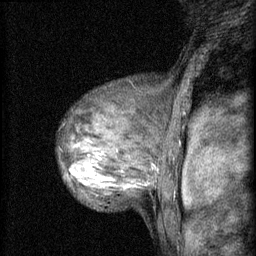
Breast MRI (dynamic contrast-enhanced), one sagittal slice. Position 46 of 60 along the scan axis. 3 images stored at this slice position (order not interpretable as contrast timing). 1.5 T. TE 4.2 ms, TR 8.2 ms. 256 × 256 image matrix, field of view 180 × 180 mm. Patient: female, 48 years.
Annotated regions visible in this slice (semi-automatic segmentation, software-assisted and operator-edited):
- analysis volume of interest (the breast-tissue region the enhancement analysis was run in; not a lesion): bounding box (x1, y1, x2, y2) in pixels: (60, 138, 133, 191)
- tumour enhancement mask (voxels above the 70 % enhancement threshold inside the analysis volume of interest): (70, 156, 131, 187)